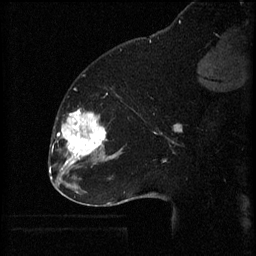
Breast MRI (dynamic contrast-enhanced), one sagittal slice. Position 21 of 60 along the scan axis. 3 images stored at this slice position (order not interpretable as contrast timing). 1.5 T. TE 4.2 ms, TR 8.2 ms. 2 mm slice thickness. 256 × 256 image matrix, field of view 180 × 180 mm. Female patient, age 32 years.
Outlined on this slice (semi-automatically segmented with operator editing):
- analysis volume of interest (the breast-tissue region the enhancement analysis was run in; not a lesion): bounding box (x1, y1, x2, y2) in pixels: (58, 108, 111, 165)
- tumour enhancement mask (voxels above the 70 % enhancement threshold inside the analysis volume of interest): (62, 108, 106, 165)